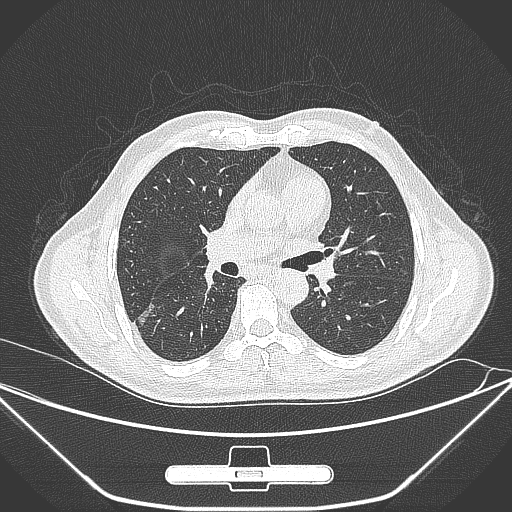
Chest CT, one axial slice; position 158 of 309 along the scan axis; lung window (W 1500 / L -600 HU); 512 × 512 image matrix, field of view 398 × 398 mm. Patient: male, 71 years. From the clinical record (not read from this slice): clinical TNM (as recorded): T1c N0 M0.
Outlined on this slice (rectangle marked by the reading radiologist):
- lung tumour (recorded histology: adenocarcinoma): bounding box <134,298,163,330> (left, top, right, bottom; pixels)